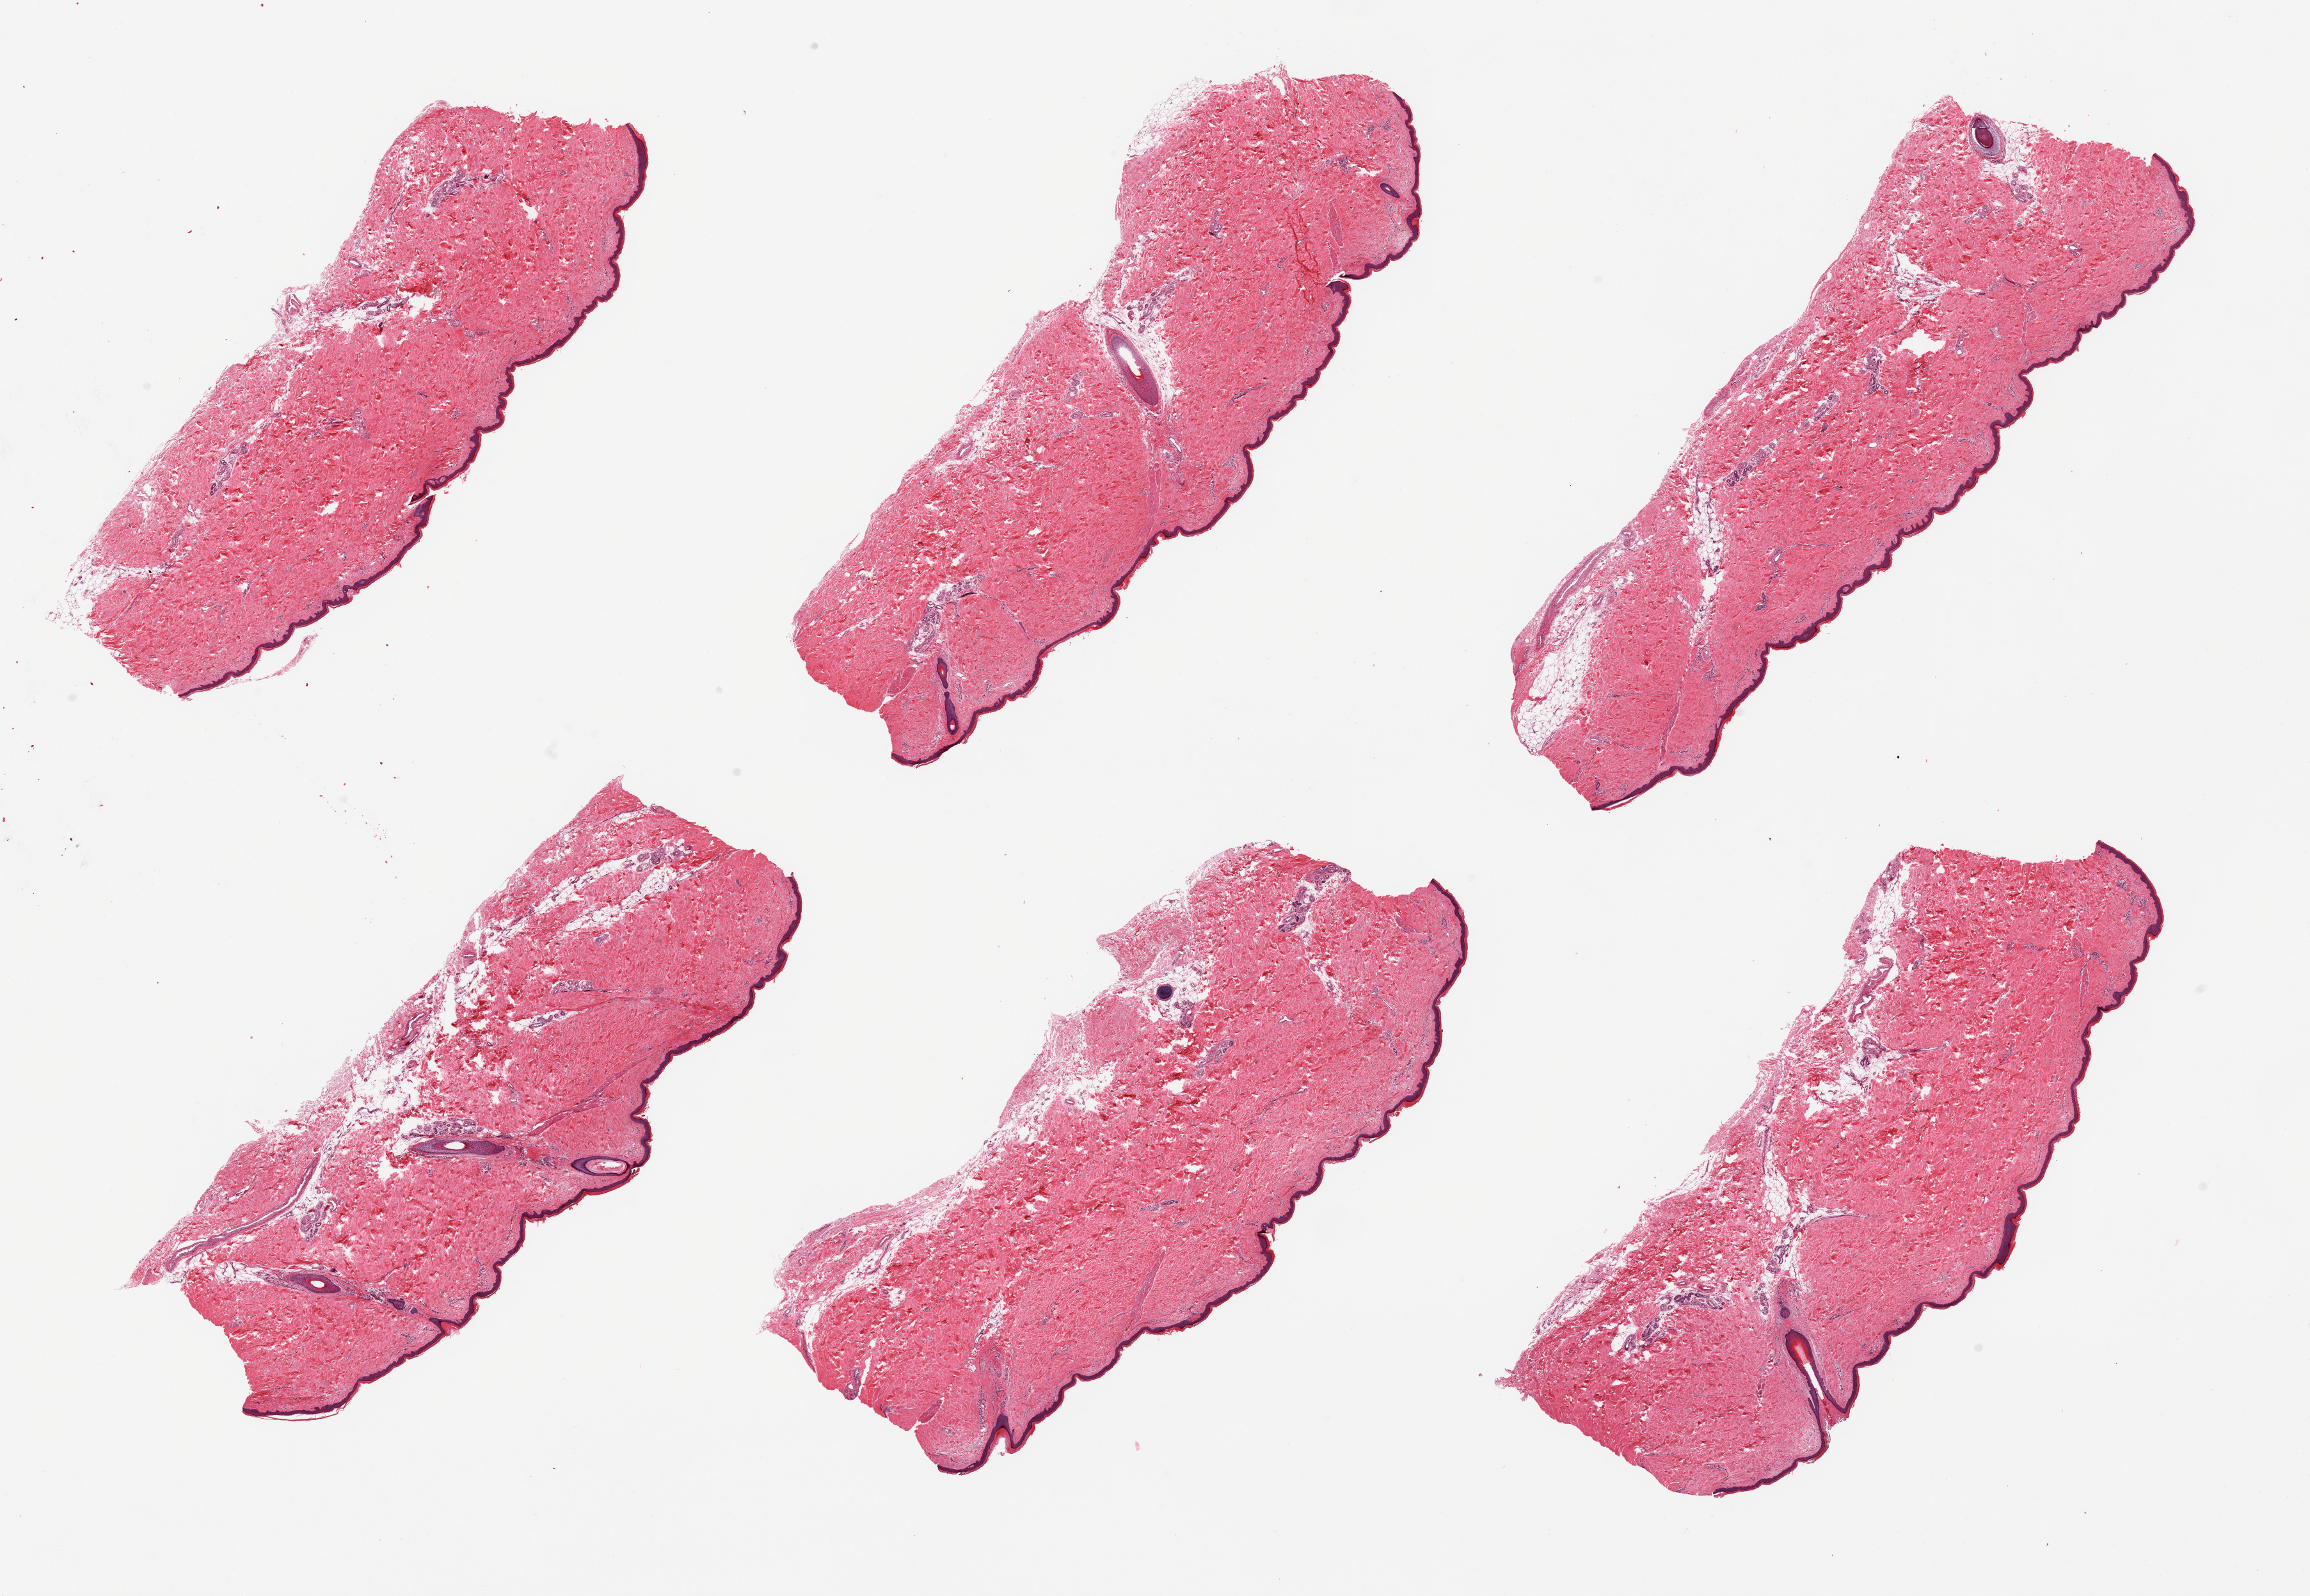
Whole-slide image, H&E stain, brightfield, shown as a low-resolution overview of the whole scanned area (about 28.5 x 19.7 mm); PAXgene-fixed paraffin-embedded (PFPE) section; section of skin of lower leg (target tissue); donor tissue sample. Donor sex: male.
* reviewer comment on this tissue sample: 6 pieces; well trimmed; 10% dermal fat